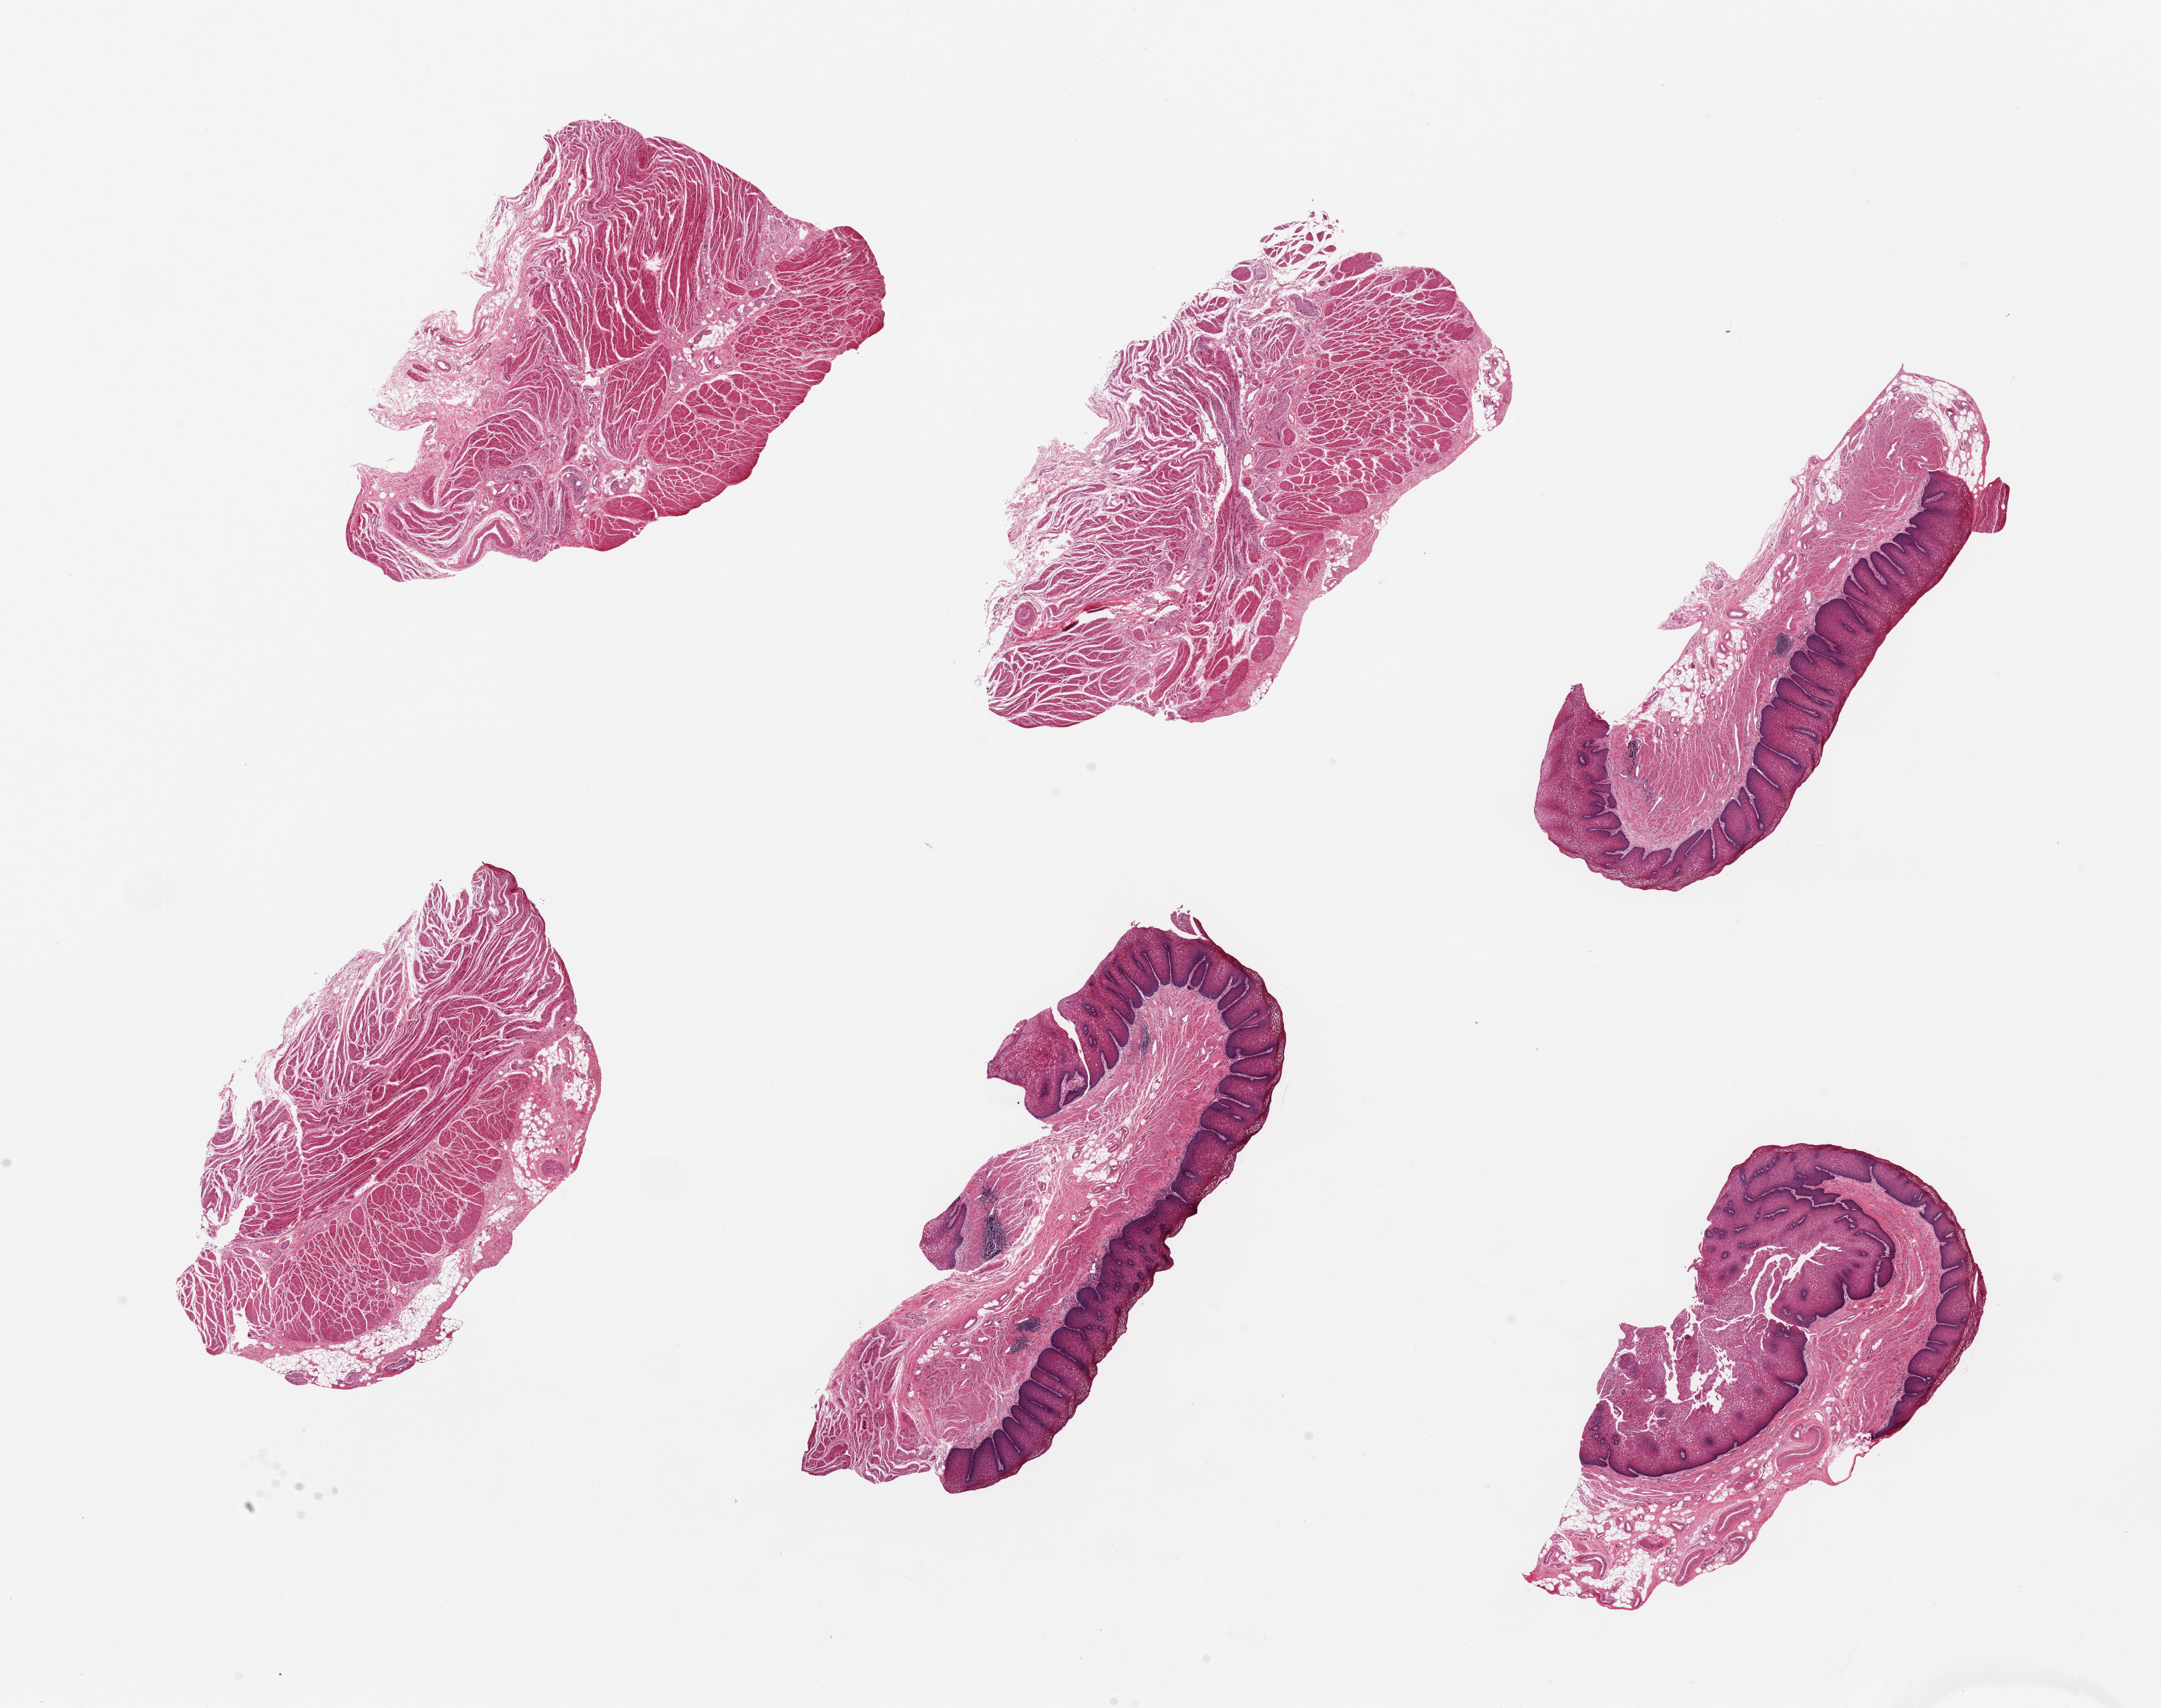
Whole-slide image, hematoxylin and eosin (H&E) stain — a low-resolution overview of the entire scanned area, about 25.6 x 20.2 mm (from a 20x scan), PAXgene-fixed, paraffin-embedded tissue, sampled site (target tissue): gastroesophageal junction, donor tissue sample. Donor: male.
- pathologist's review note for this sample: 6 pieces, 3 with mucosa (not target) and no muscle (target), 3 comprised of muscle